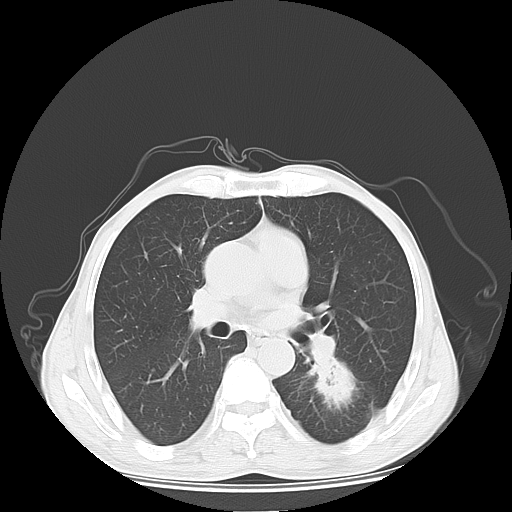
Chest CT, one axial slice; slice 35 of 65 in the series (ordered by position); reconstruction kernel LUNG; 120 kVp; lung window (W 1500 / L -600 HU); 5 mm slice thickness; 512 × 512 image matrix, field of view 350 × 350 mm. Male patient, age 63 years. From the clinical record (not read from this slice): clinical TNM (as recorded): T1c N0 M1b.
Structures marked on this image (bounding box drawn by a radiologist):
- lung tumour (recorded histology: adenocarcinoma): bounding box (x1, y1, x2, y2) in pixels: (302, 348, 366, 412)